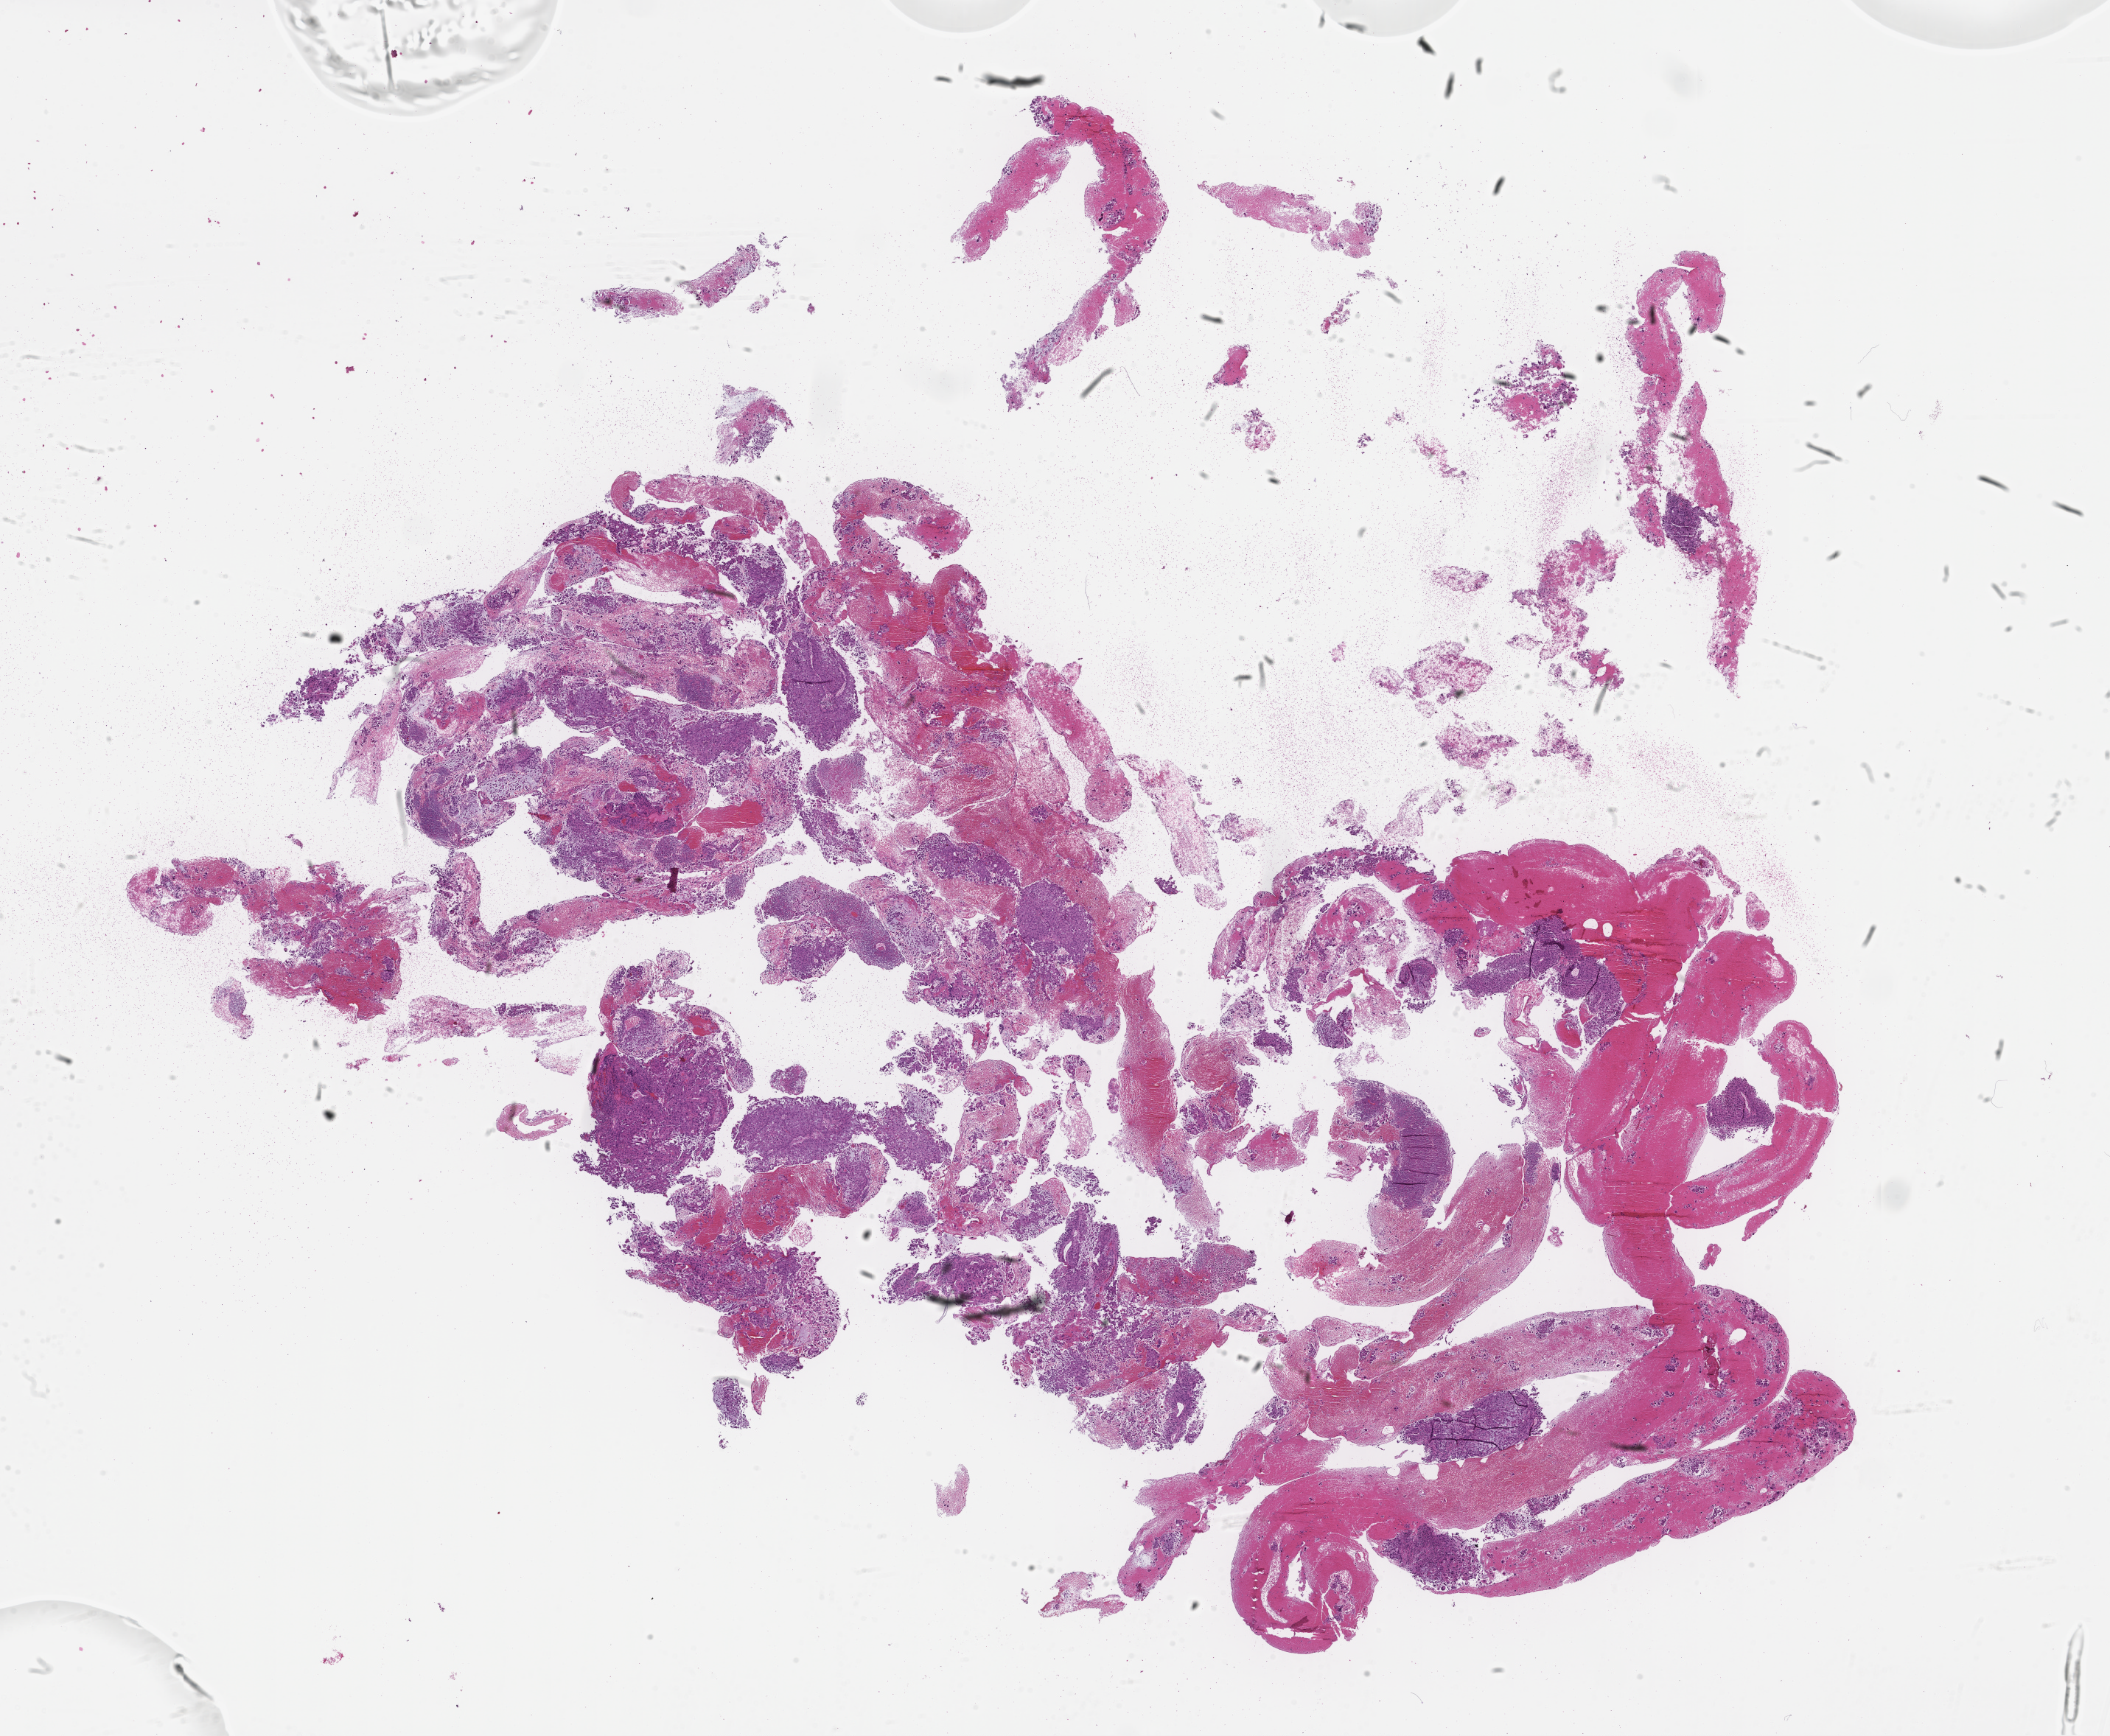
Digitized H&E-stained section — low-resolution overview of the scanned area, about 23.1 x 19.0 mm, FFPE section, tissue site: lung. Patient sex: male.
This section: primary tumor. Diagnosis: Non-Small Cell Lung Carcinoma.